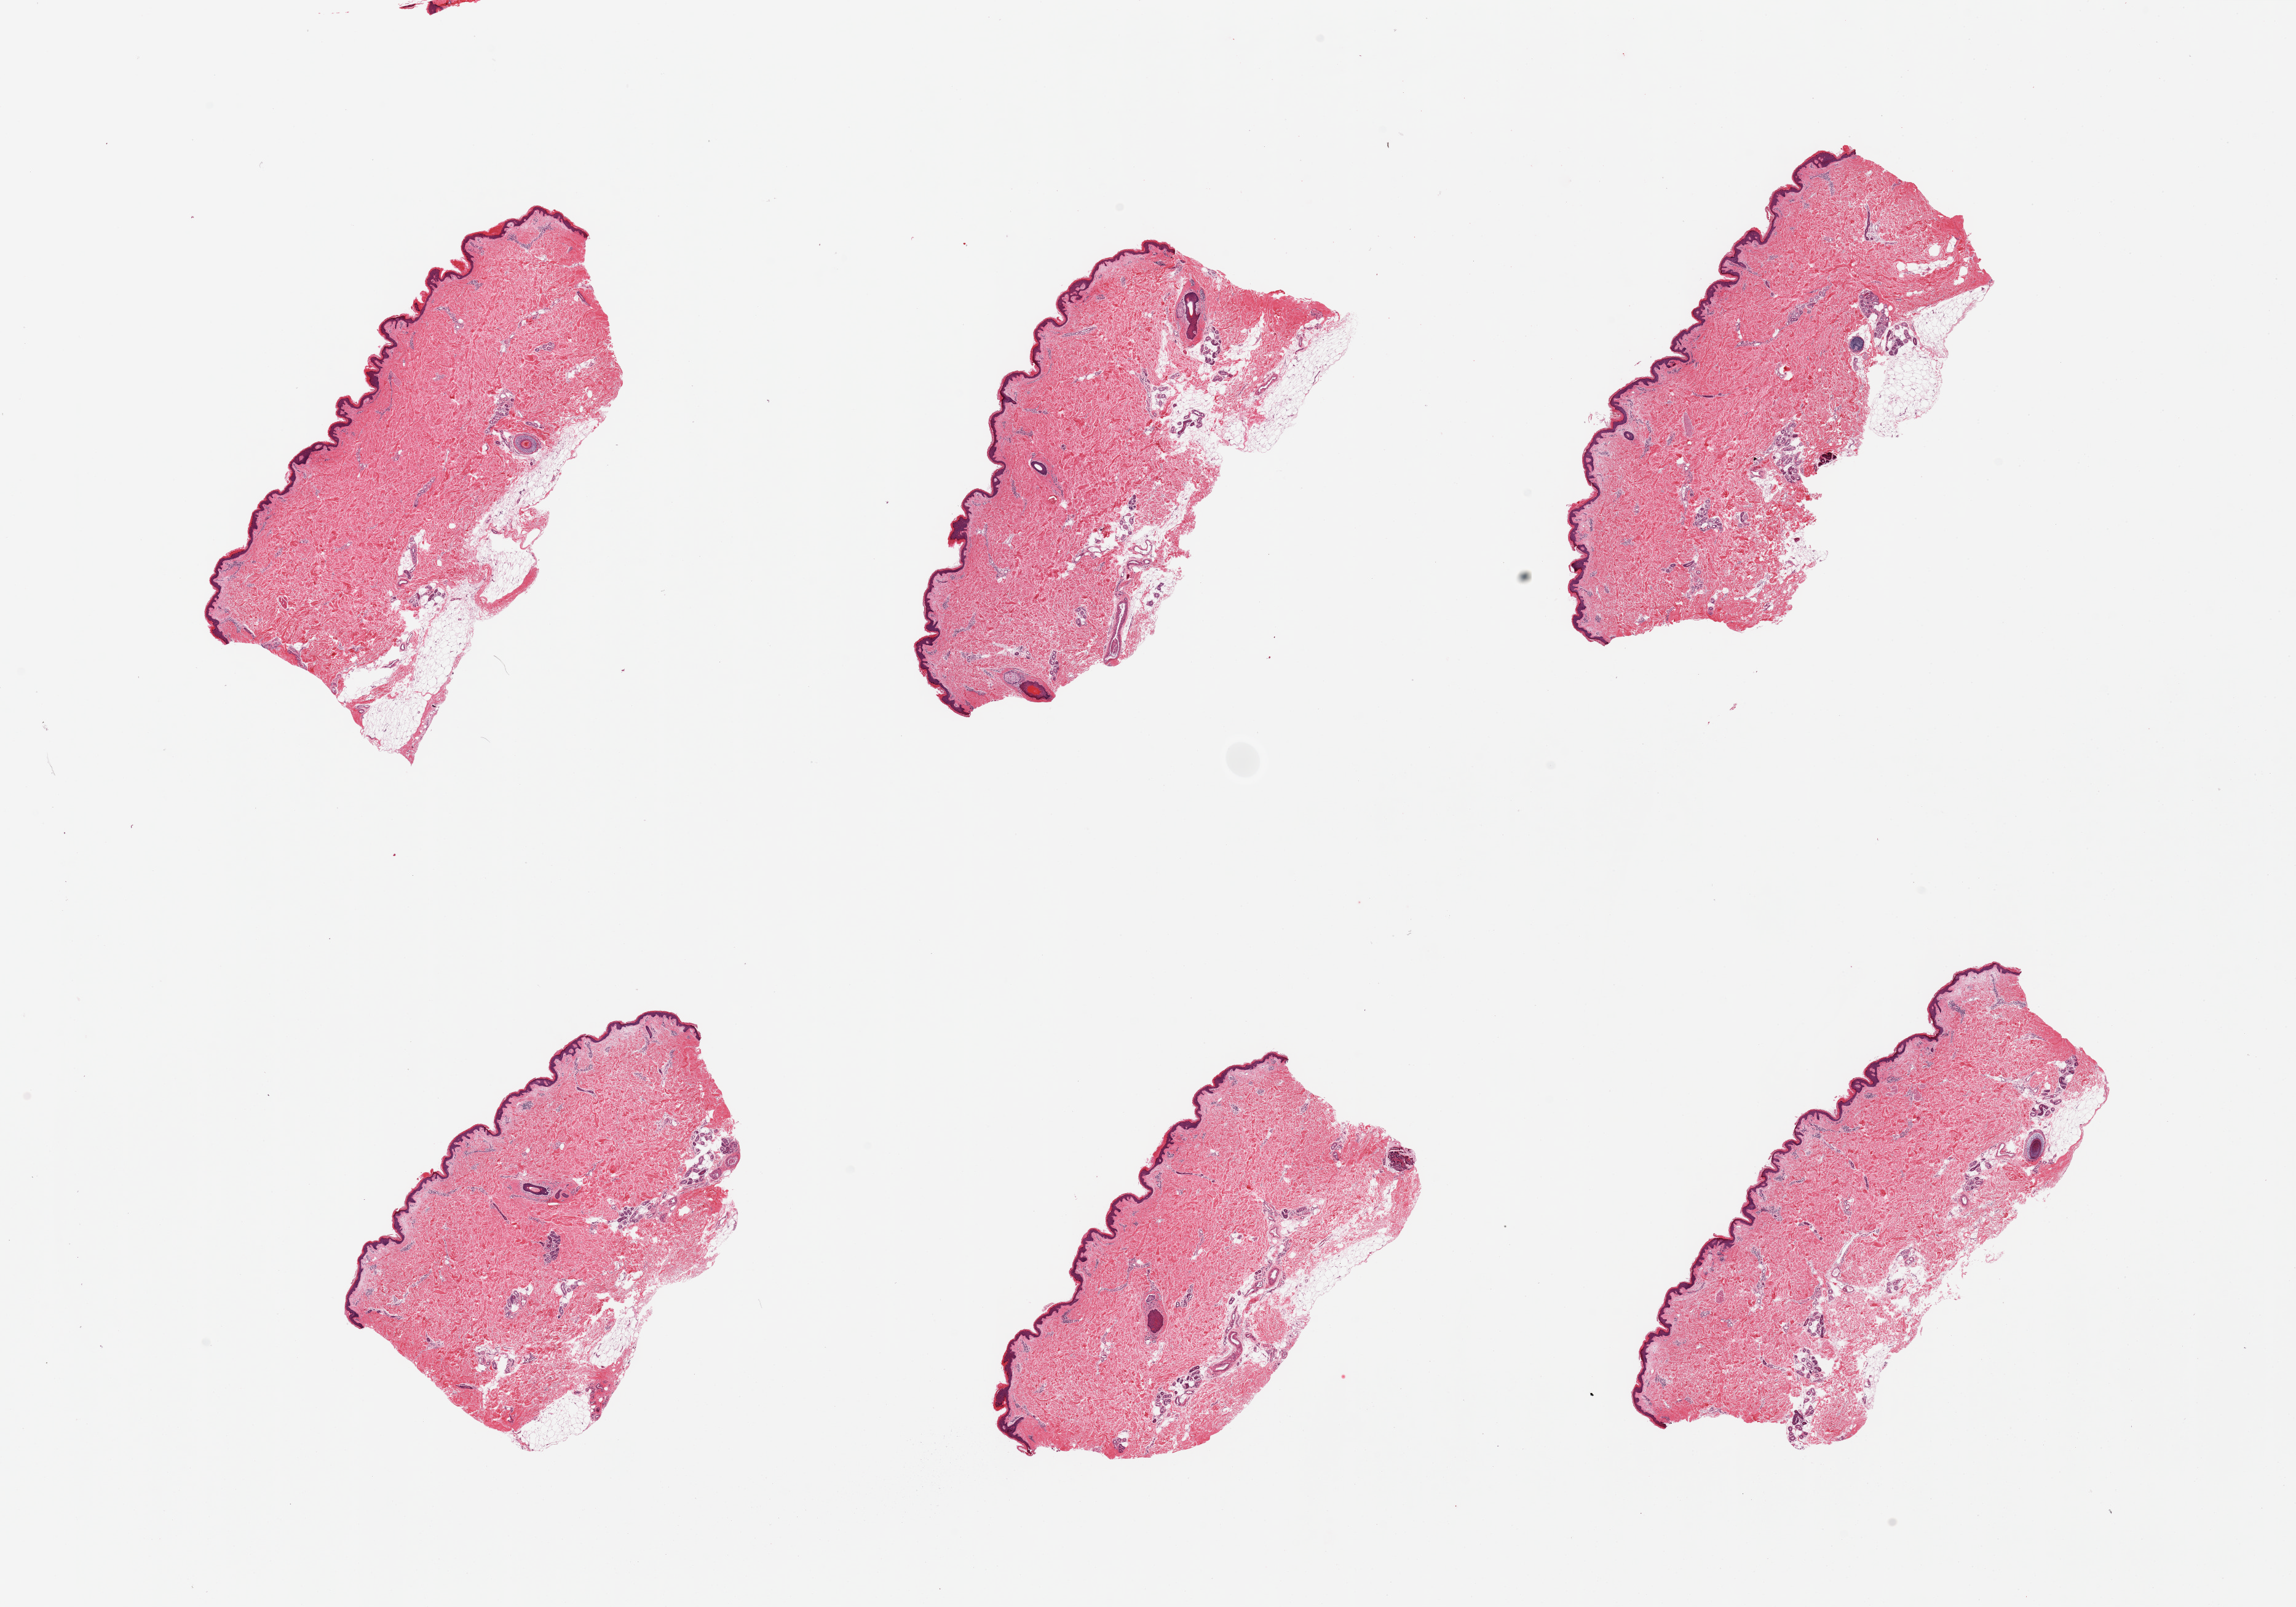
Haematoxylin and eosin whole-slide image, low-resolution overview of the scanned area, about 29.5 x 20.7 mm. PAXgene-fixed paraffin-embedded (PFPE) section. Sampled site (target tissue): skin of lower leg. Tissue donor sample.
Review note (as recorded): 6 pieces. Well trimmed; up to 0.5 mm fat.